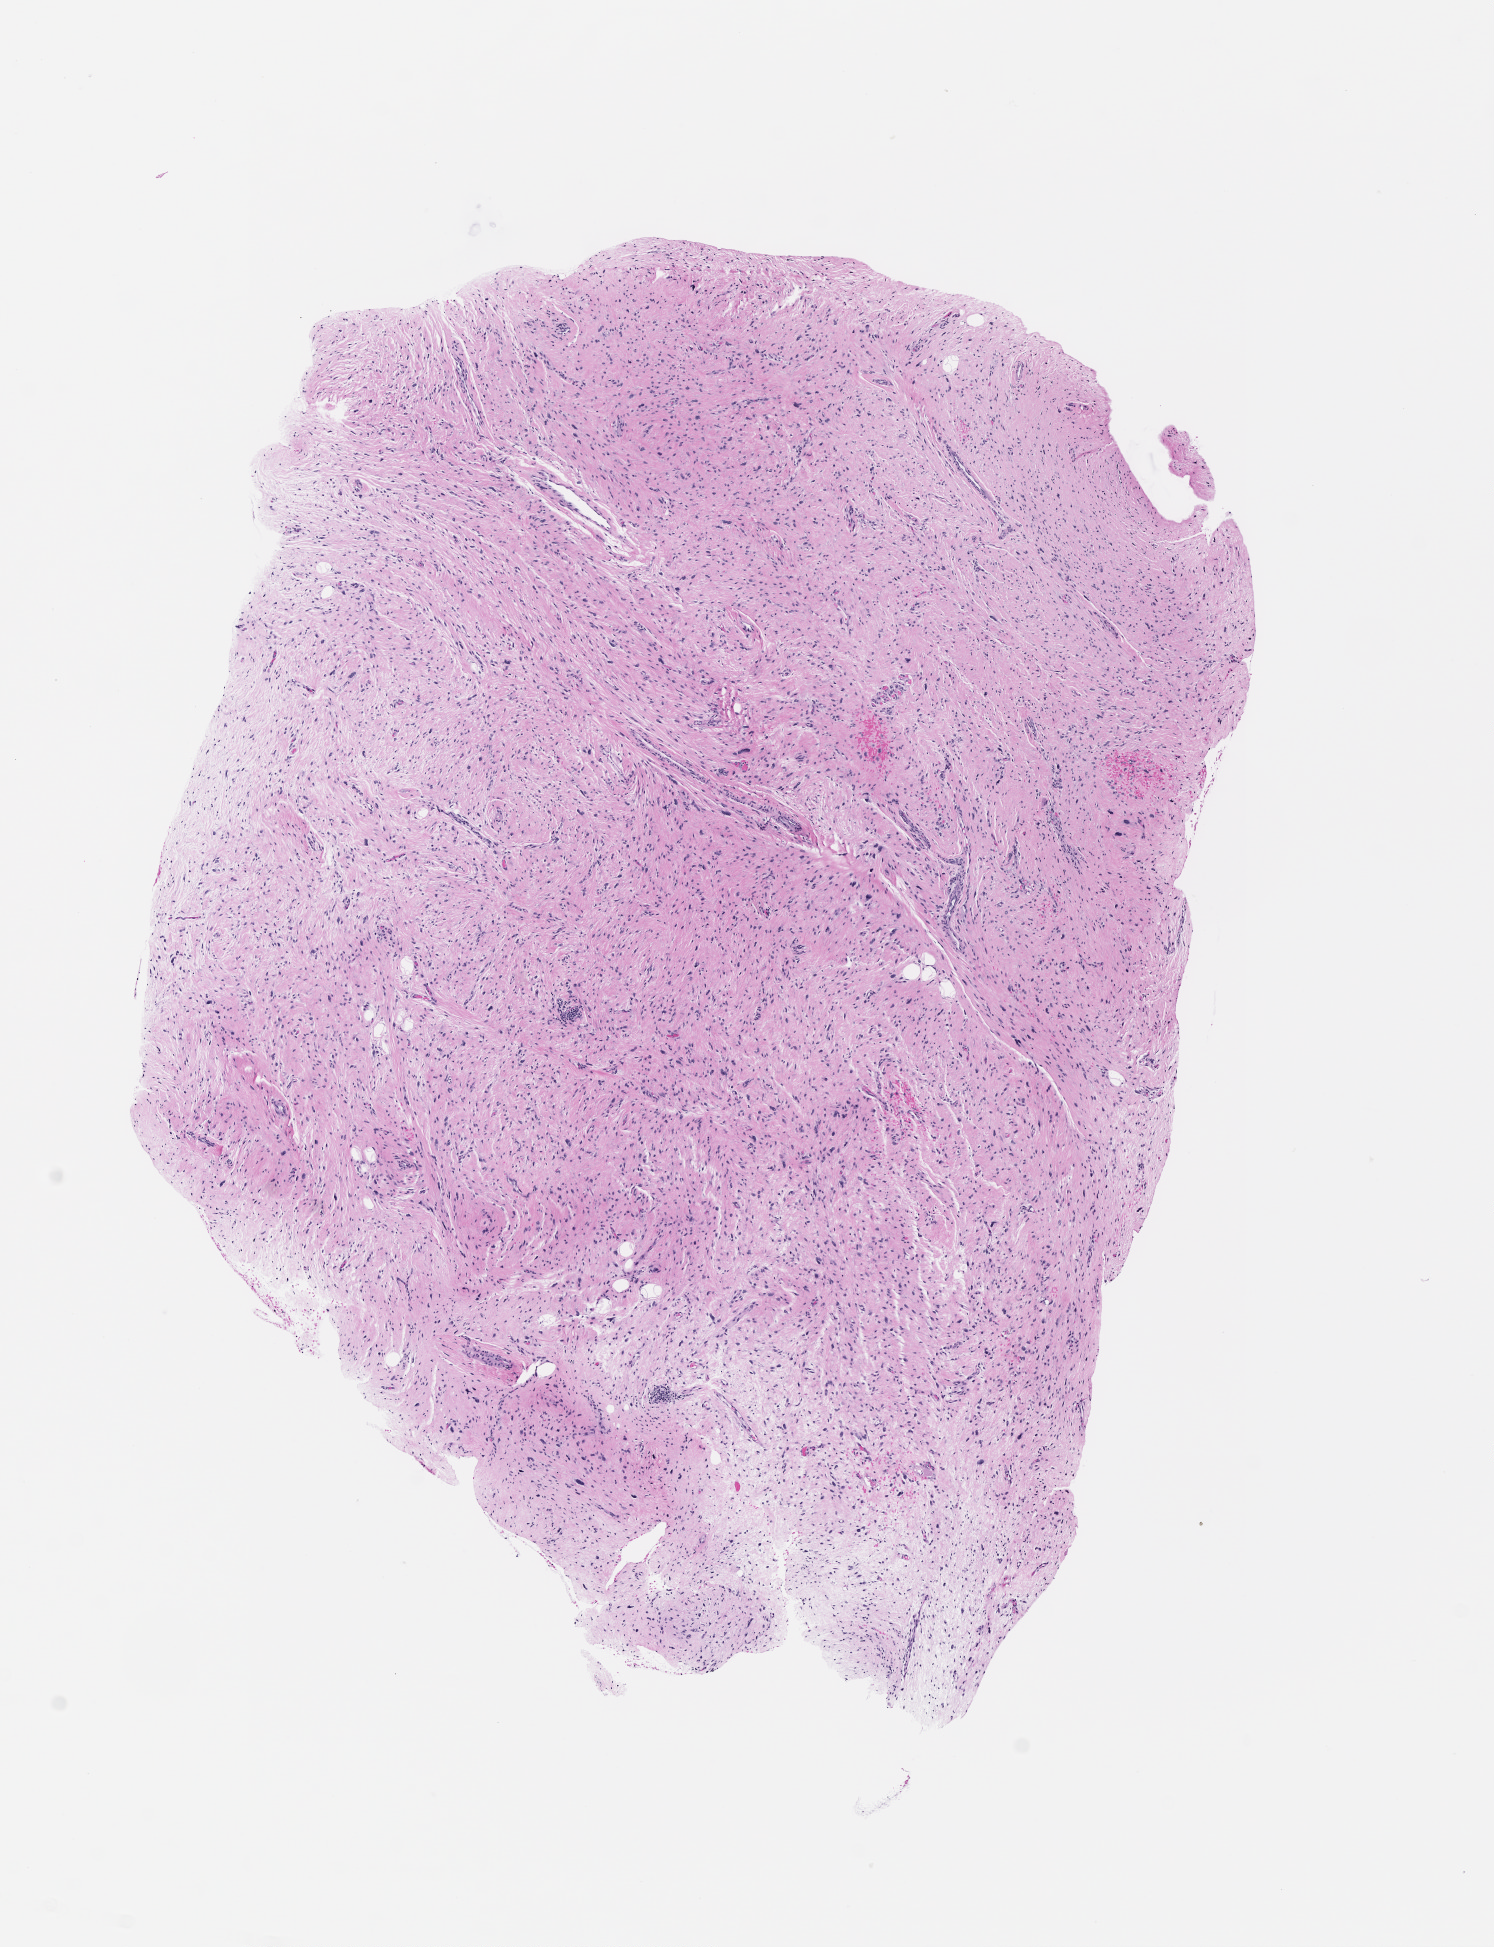
Whole-slide histology image, H&E — low-resolution overview of the scanned area, about 6.0 x 7.8 mm.
* patient diagnosis (cohort enrolment): sarcoma (site not recorded at cohort level)